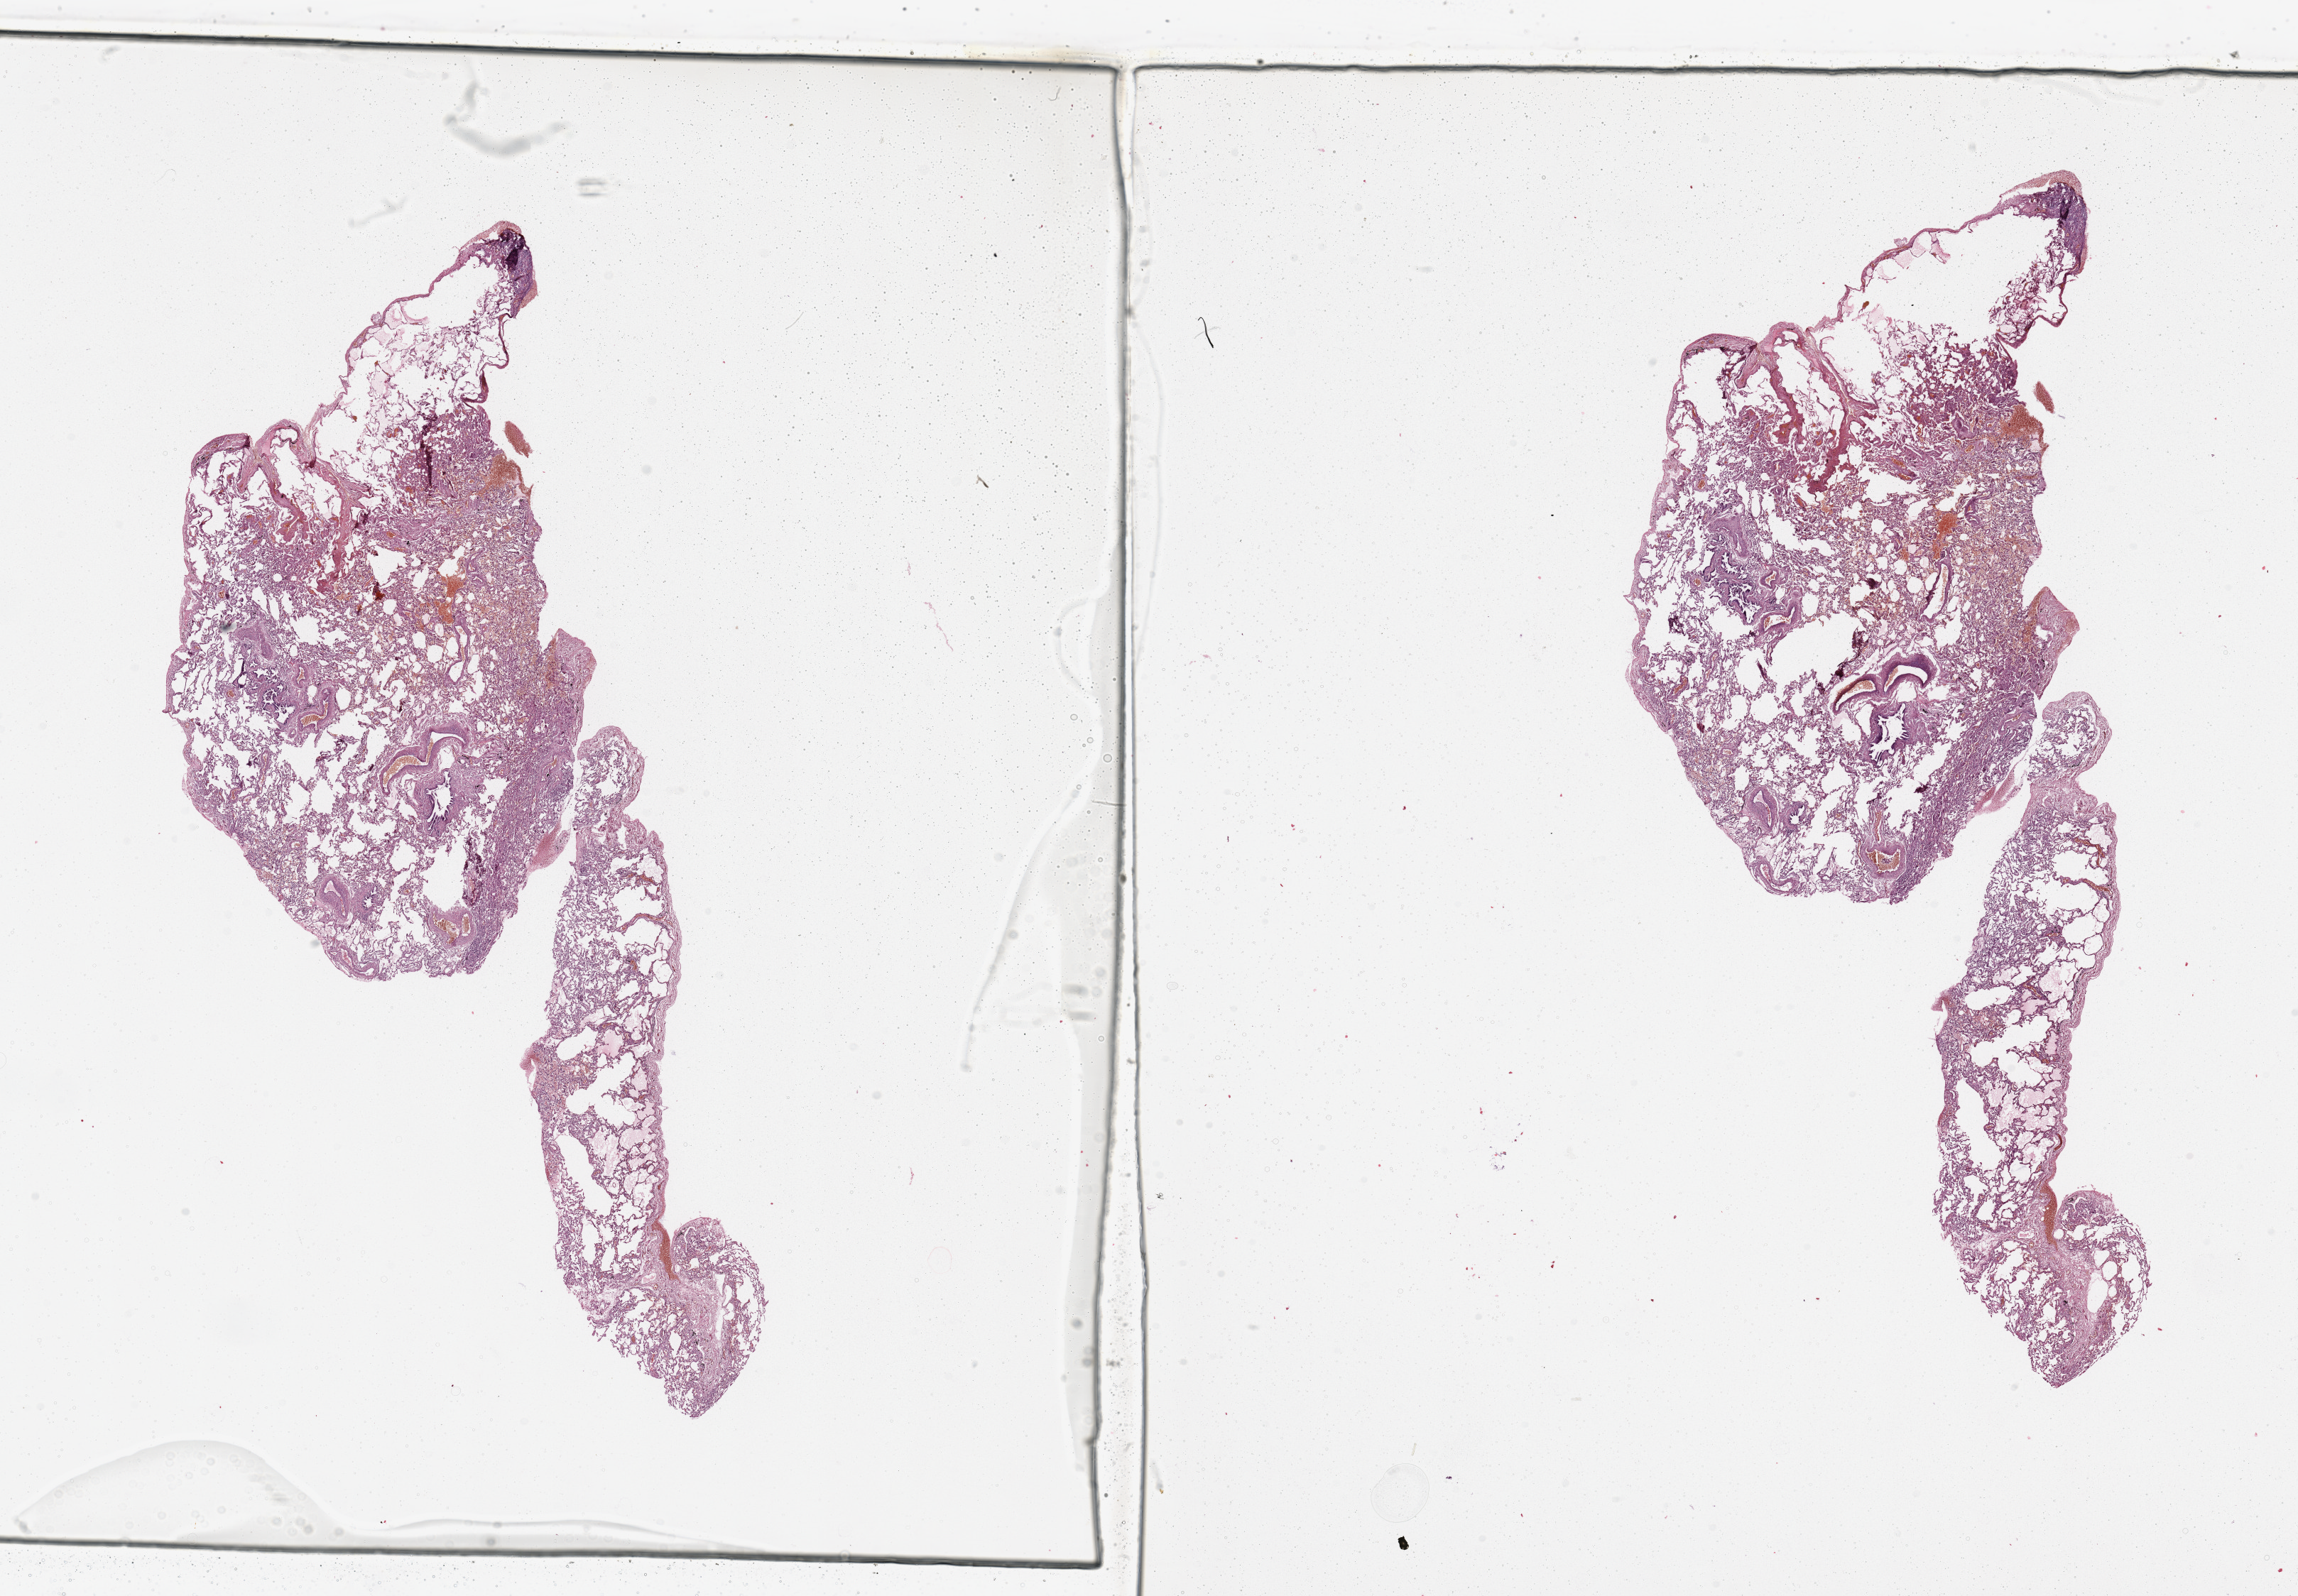
H&E whole-slide image, a low-resolution overview of the entire scanned area, about 25.6 x 17.8 mm (acquisition: 20x scan). Normal (non-tumour) tissue sample, sampled site: lung. Female, 63 y/o.
This section: normal (non-tumour) tissue from the same patient. Patient diagnosis: Adenocarcinoma, NOS.